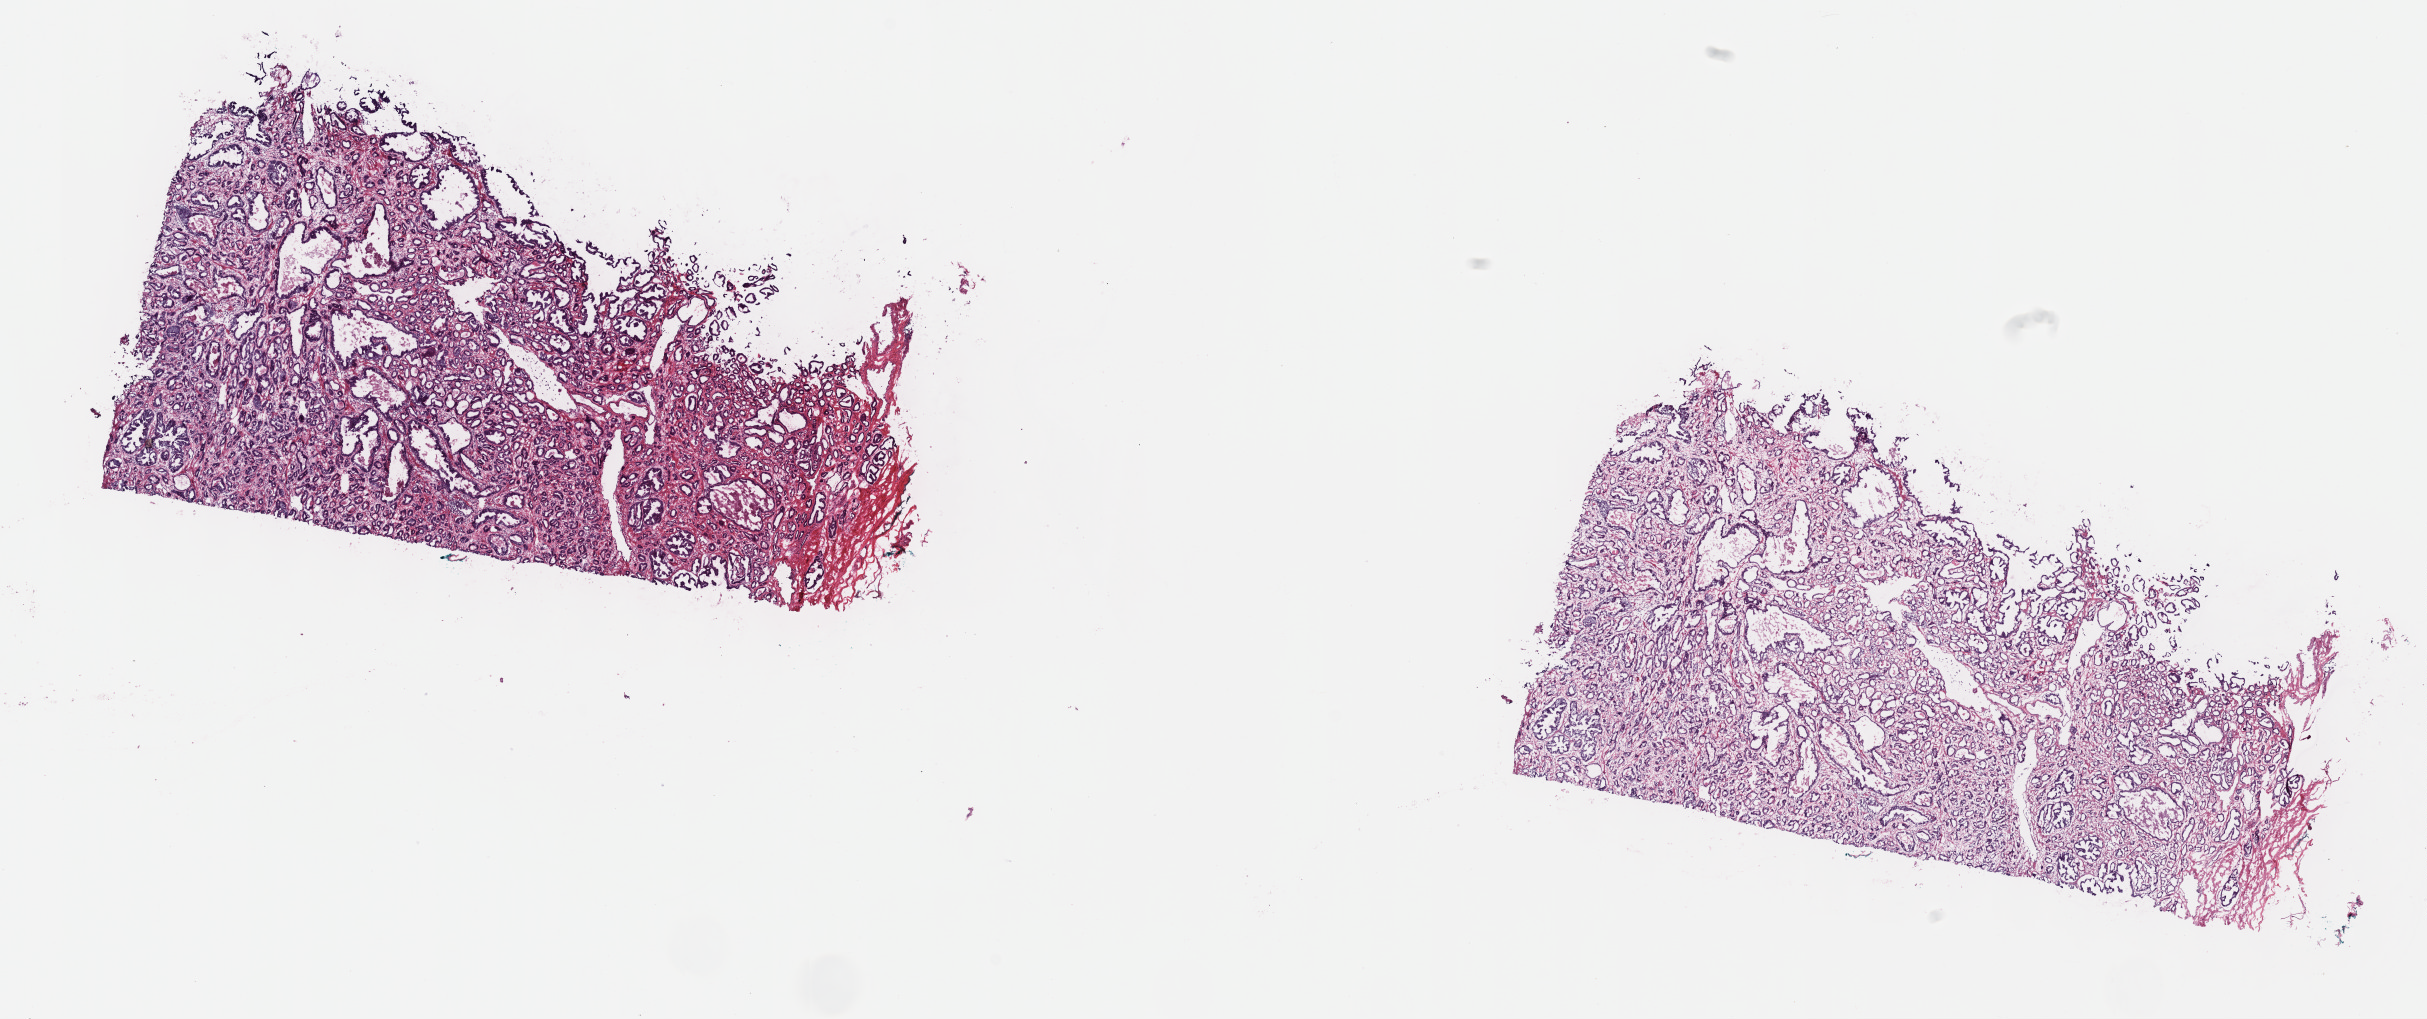
Whole-slide histology image, H&E-stained — shown as a low-resolution overview of the whole scanned area (about 19.6 x 8.2 mm, acquisition: 40x scan); frozen section from the top of the tissue portion; sample: primary tumour, prostate. Patient: male, age at initial diagnosis 62 years. Gleason score: 7 (3+4). Slide review estimates, as recorded: tumour cells 70%, tumour nuclei 70%, normal cells 0%, stromal cells 30%, necrosis 0%. Inflammatory infiltration, as recorded: lymphocyte infiltration 40%, monocyte infiltration 20%, neutrophil infiltration 20%.
Lymph nodes positive (case pathology): 0 of 16 examined. Laterality: bilateral. Pathologic diagnosis: Adenocarcinoma, NOS (prostate gland).